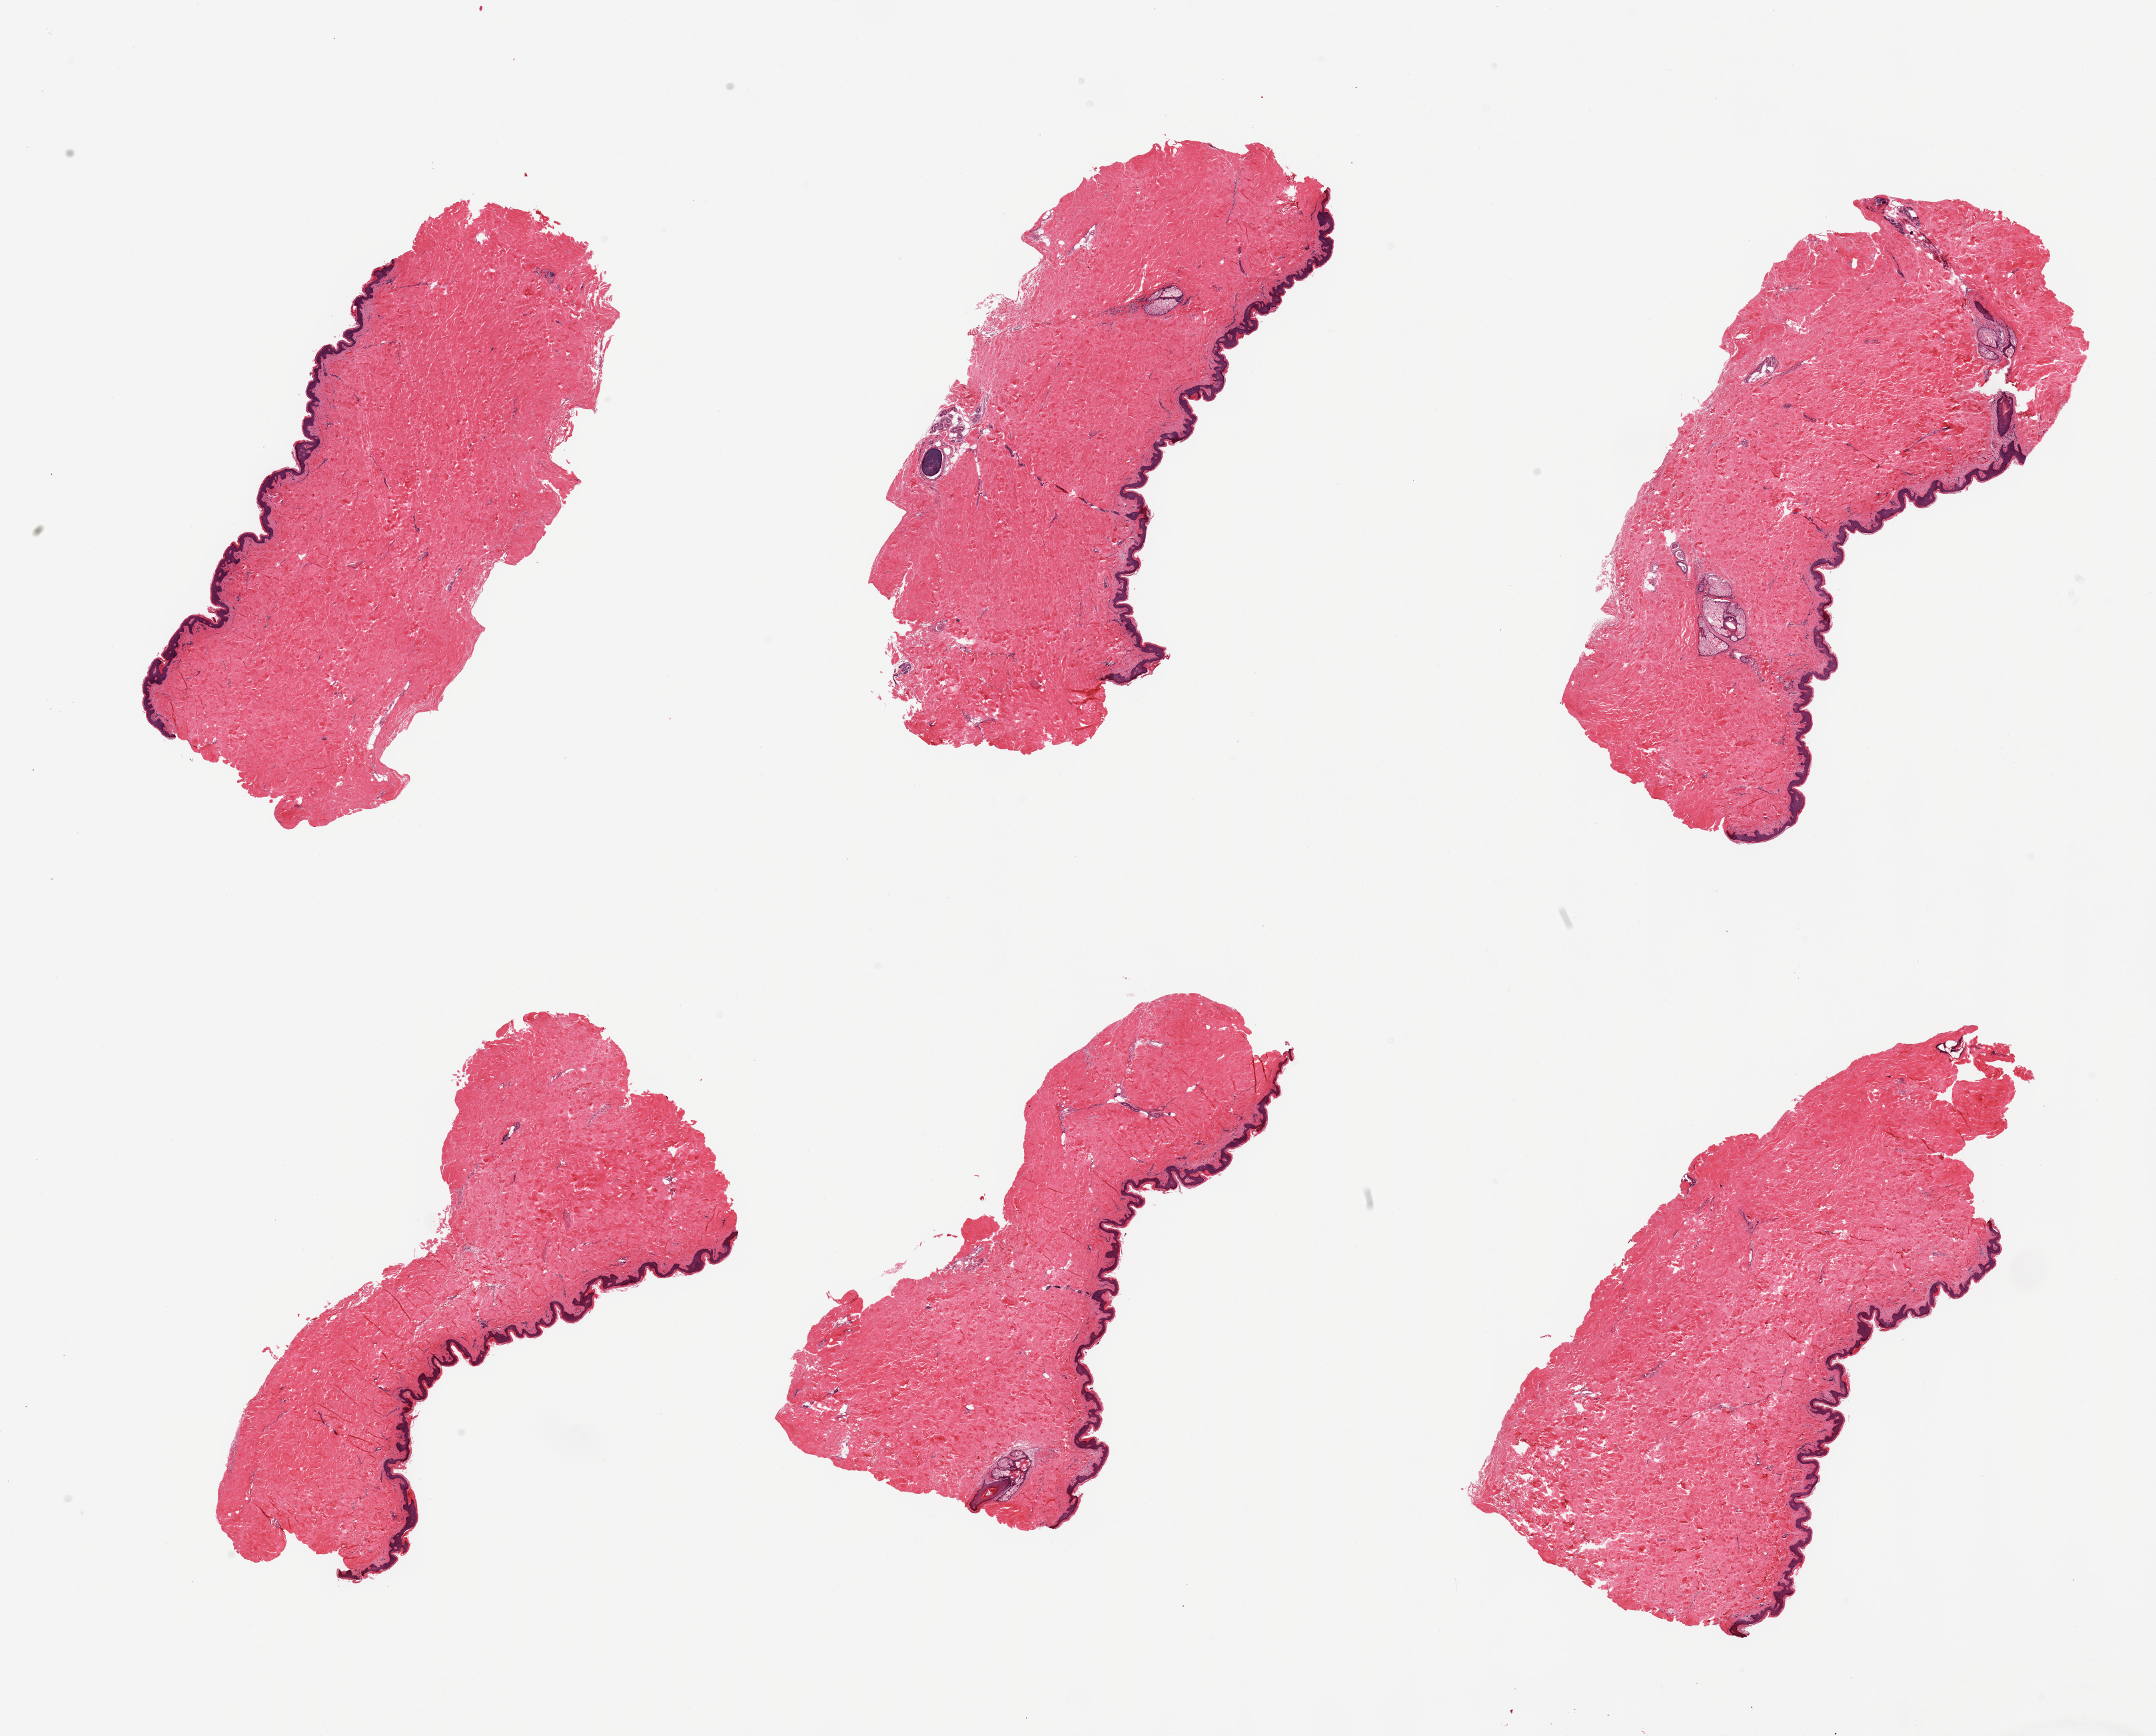
Whole-slide image, hematoxylin and eosin (H&E) stain, brightfield — a low-resolution overview of the entire scanned area, about 25.6 x 20.6 mm, PAXgene-fixed, paraffin-embedded tissue, sampled site (target tissue): skin of suprapubic region, donor tissue sample. Male donor.
Pathologist's review note for this sample: 6 pieces; well trimmed.